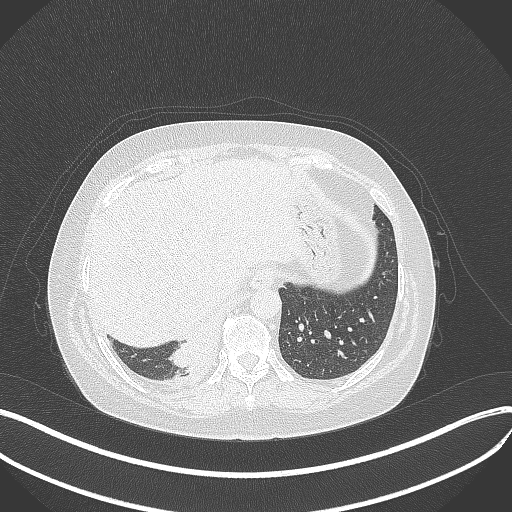
Chest CT, one axial slice; slice 80 of 381 in the series (ordered by position); reconstruction kernel B70f; 120 kVp; lung window (W 1500 / L -600 HU); 1 mm slice thickness; 512 × 512 image matrix, field of view 400 × 400 mm. Patient: female, 56 years. From the clinical record (not read from this slice): clinical TNM (as recorded): T2b N1 M0.
Annotated regions visible in this slice (bounding box drawn by a radiologist):
- lung tumour (recorded histology: small cell carcinoma): bounding box <173,323,221,373> (left, top, right, bottom; pixels)